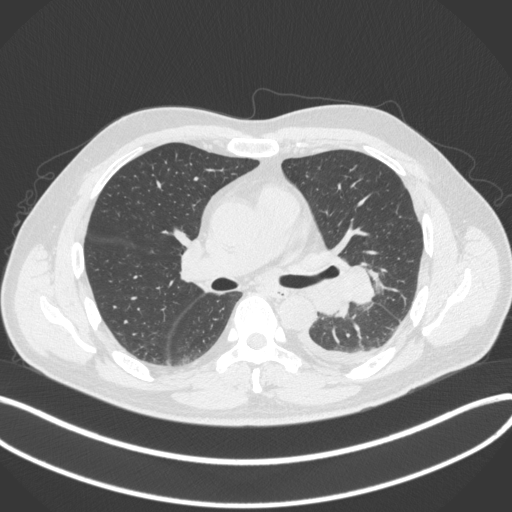
Chest CT, one axial slice; position 210 of 350 along the scan axis; reconstruction kernel B31f; 120 kVp; lung window (W 1500 / L -600 HU); 1 mm slice thickness; 512 × 512 image matrix. Male patient, age 58 years. From the clinical record (not read from this slice): clinical TNM (as recorded): T3 N1 M1b; histopathological grade: G3.
Outlined on this slice (rectangle marked by the reading radiologist):
- lung tumour (recorded histology: small cell carcinoma): bounding box <308,261,376,314> (left, top, right, bottom; pixels)